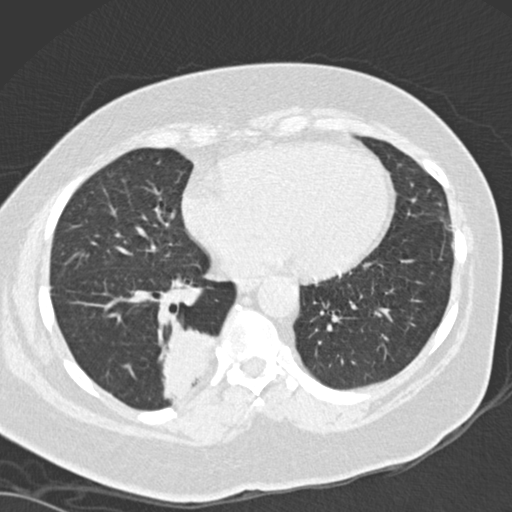
Low-dose screening chest CT, axial slice; baseline screening round; lung window (W 1500 / L -600 HU); 2 mm slice thickness; 120 kVp; 512 × 512 image matrix. Female participant, aged 66 years at enrolment. Current smoker at enrolment.
• Expert-annotated lung lesion, bounding box [x1, y1, x2, y2] px = [147, 317, 231, 404].
• The screening reader recorded 3 non-calcified nodules or masses ≥4 mm on this exam (left lower lobe, left lower lobe, right lower lobe); which of them this box marks is not recorded.
• Official screen result: positive, change unspecified: nodule(s) >= 4 mm or enlarging nodule(s), mass(es), or other non-specific abnormalities suspicious for lung cancer.
• Lung cancer was diagnosed 67 days after this screen: adenocarcinoma, NOS, right lower lobe, well differentiated (G1), stage IB (AJCC 6th edition), 55 mm at pathology.